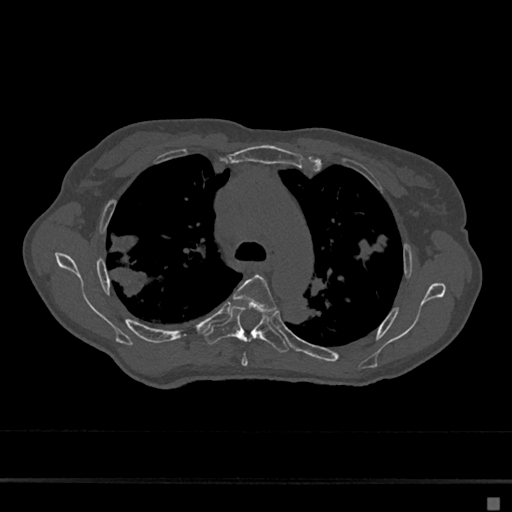
CT including the spine, one axial slice; 120 kVp; bone window (W 1800 / L 400 HU); 0.5 mm slice thickness; 512 × 512 image matrix, field of view 360 × 360 mm. Patient: female, 68 years. From the clinical record (not read from this slice): primary cancer: renal.
Outlined on this slice (semi-automatically segmented with operator editing):
- T4 vertebra: bounding box (x1, y1, x2, y2) in pixels: (233, 275, 277, 367)
- T5 vertebra: (205, 305, 289, 353)